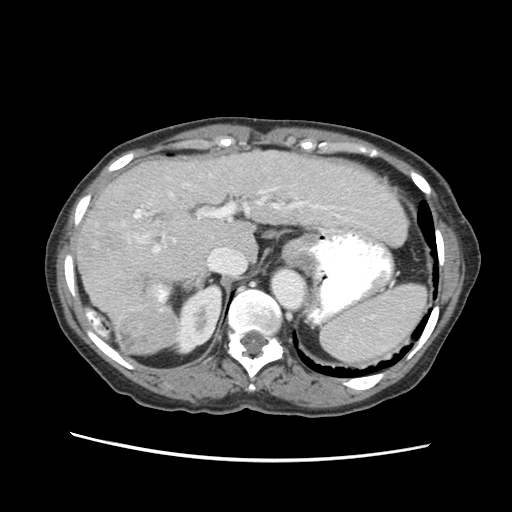
Contrast-enhanced abdominal CT (liver protocol), one axial slice; position 42 of 63 along the scan axis; soft-tissue window (W 400 / L 40 HU); 2.5 mm slice thickness; 512 × 512 image matrix. From the clinical record (not read from this slice): diagnosis: hepatocellular carcinoma (patient treated with transarterial chemoembolisation; whether this scan precedes or follows treatment is not stated here); TNM stage (as recorded): Stage-I; Child-Pugh class: B; tumour differentiation: well differentiated; tumour nodularity: uninodular.
Structures marked on this image (semi-automatically segmented with operator editing):
- liver parenchyma outside the tumour (the mass and vessels are separate outlines, so this box may not span the whole liver): bounding box <76,148,406,354> (left, top, right, bottom; pixels)
- mass: <111,297,179,353>
- liver vessels: <132,194,343,254>